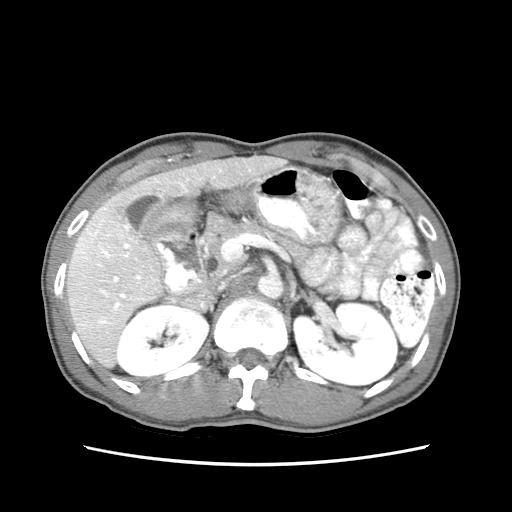
Contrast-enhanced abdominal CT (liver protocol), one axial slice. Position 33 of 79 along the scan axis. Reconstruction kernel STANDARD. Soft-tissue window (W 400 / L 40 HU). 2.5 mm slice thickness. 512 × 512 image matrix, field of view 320 × 320 mm. Case-level facts recorded for this patient, not image findings: diagnosis: hepatocellular carcinoma (patient treated with transarterial chemoembolisation; whether this scan precedes or follows treatment is not stated here); TNM stage (as recorded): Stage-IIIB; Child-Pugh class: A; tumour differentiation: moderately differentiated; tumour nodularity: multinodular.
Outlined on this slice (semi-automatic segmentation, software-assisted and operator-edited):
- liver parenchyma outside the tumour (the mass and vessels are separate outlines, so this box may not span the whole liver): bounding box [x1, y1, x2, y2] px = [66, 154, 284, 366]
- liver vessels: [78, 162, 271, 339]